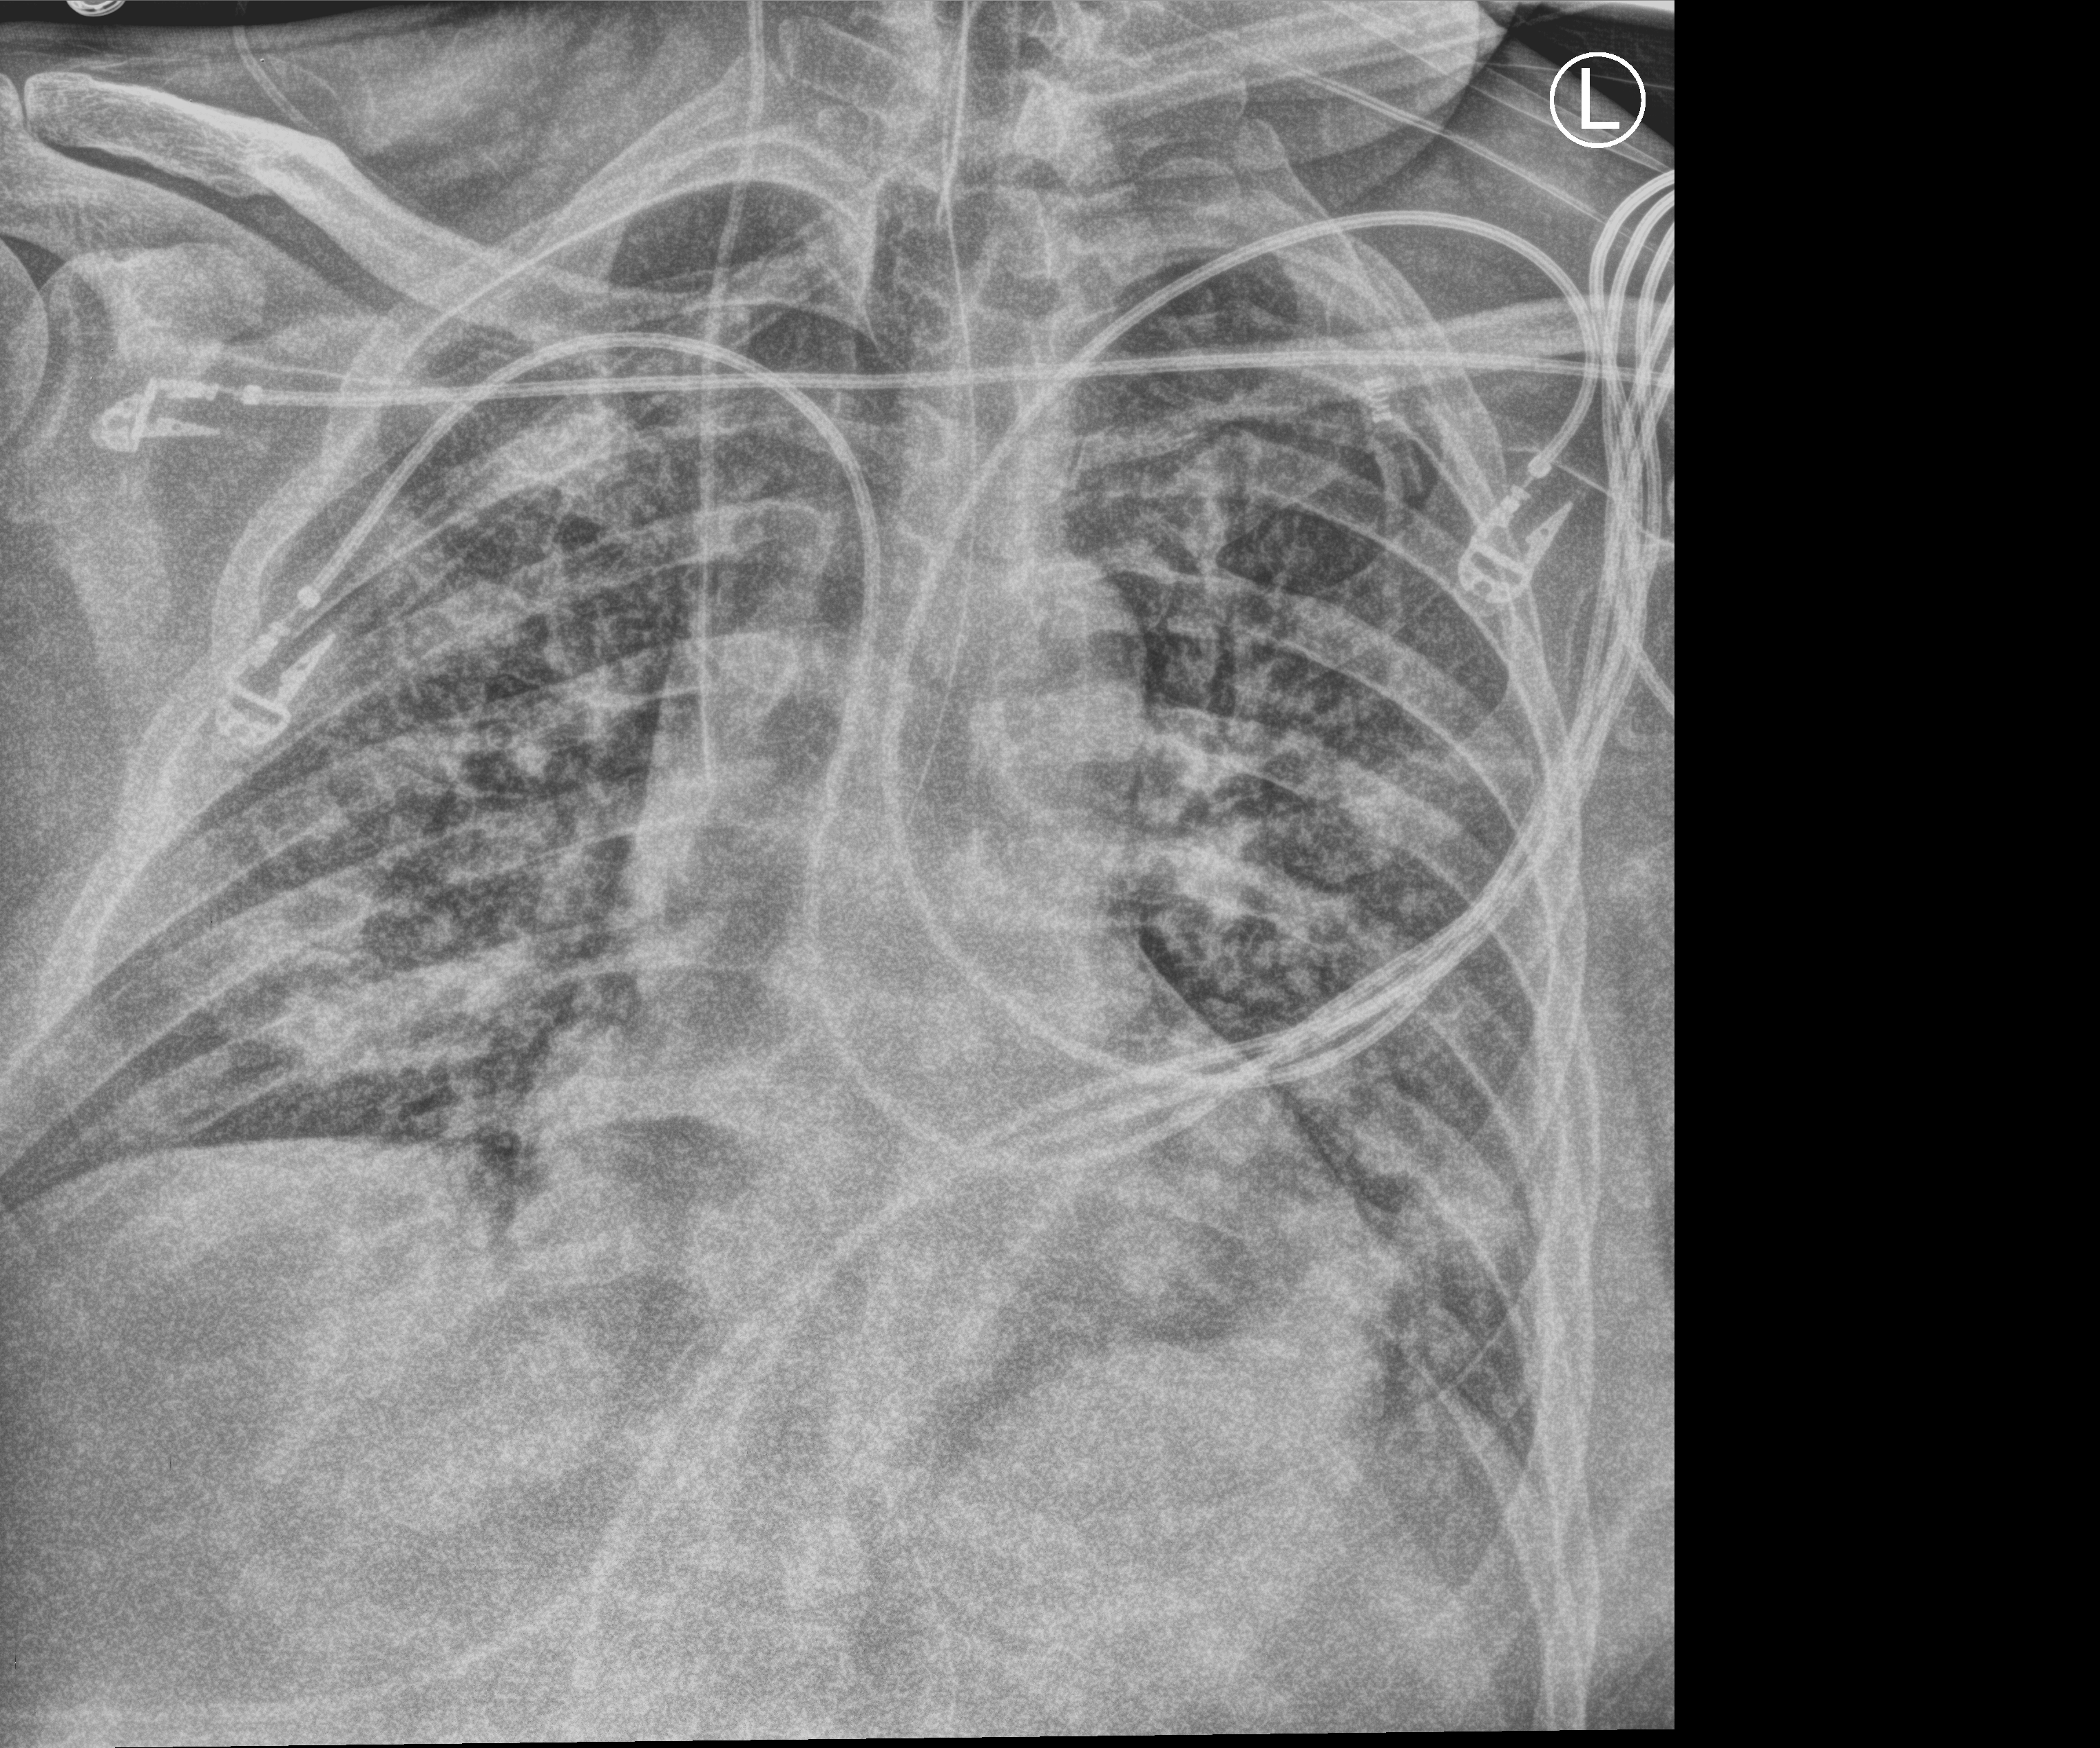
Bedside chest radiograph (computed radiography); anteroposterior (AP) projection. Patient hospitalised with COVID-19; male, aged 18–59 years.
From the hospital-stay record, not from the radiograph (when in the stay this image was taken is not recorded):
- admitted to intensive care during this hospital stay: no
- mechanically ventilated during this hospital stay: yes